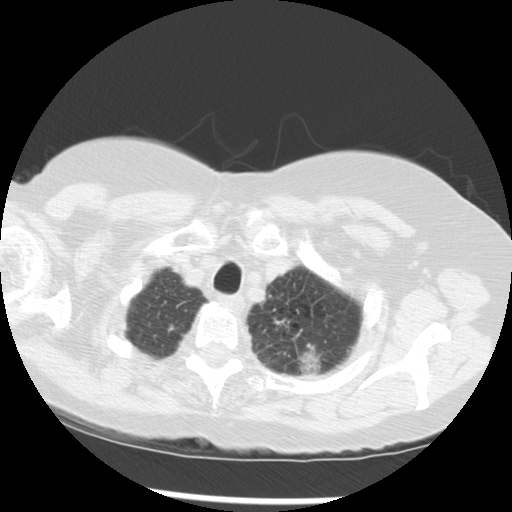
Chest CT (low-dose screening protocol), one axial image. Third screening round (two years after baseline). Lung window (W 1500 / L -600 HU). 2.5 mm slice thickness. Slice 250 of 283 in the series. Female participant, aged 70 years at enrolment.
Expert-annotated lung lesion, box from (x=242, y=298) to (x=342, y=385) px. The exam's reader record, not a measurement of the box and not confirmed to be the same lesion: non-calcified nodule or mass ≥4 mm, left upper lobe, 32 × 26 mm, spiculated (stellate) margins, soft tissue attenuation, pre-existing on the prior screen: yes; interval growth: yes. Official screen result: positive, other. Later outcome: lung cancer diagnosed 24 days after this screen — neoplasm, malignant, left upper lobe, stage IIIB (AJCC 6th edition), 40 mm at pathology.